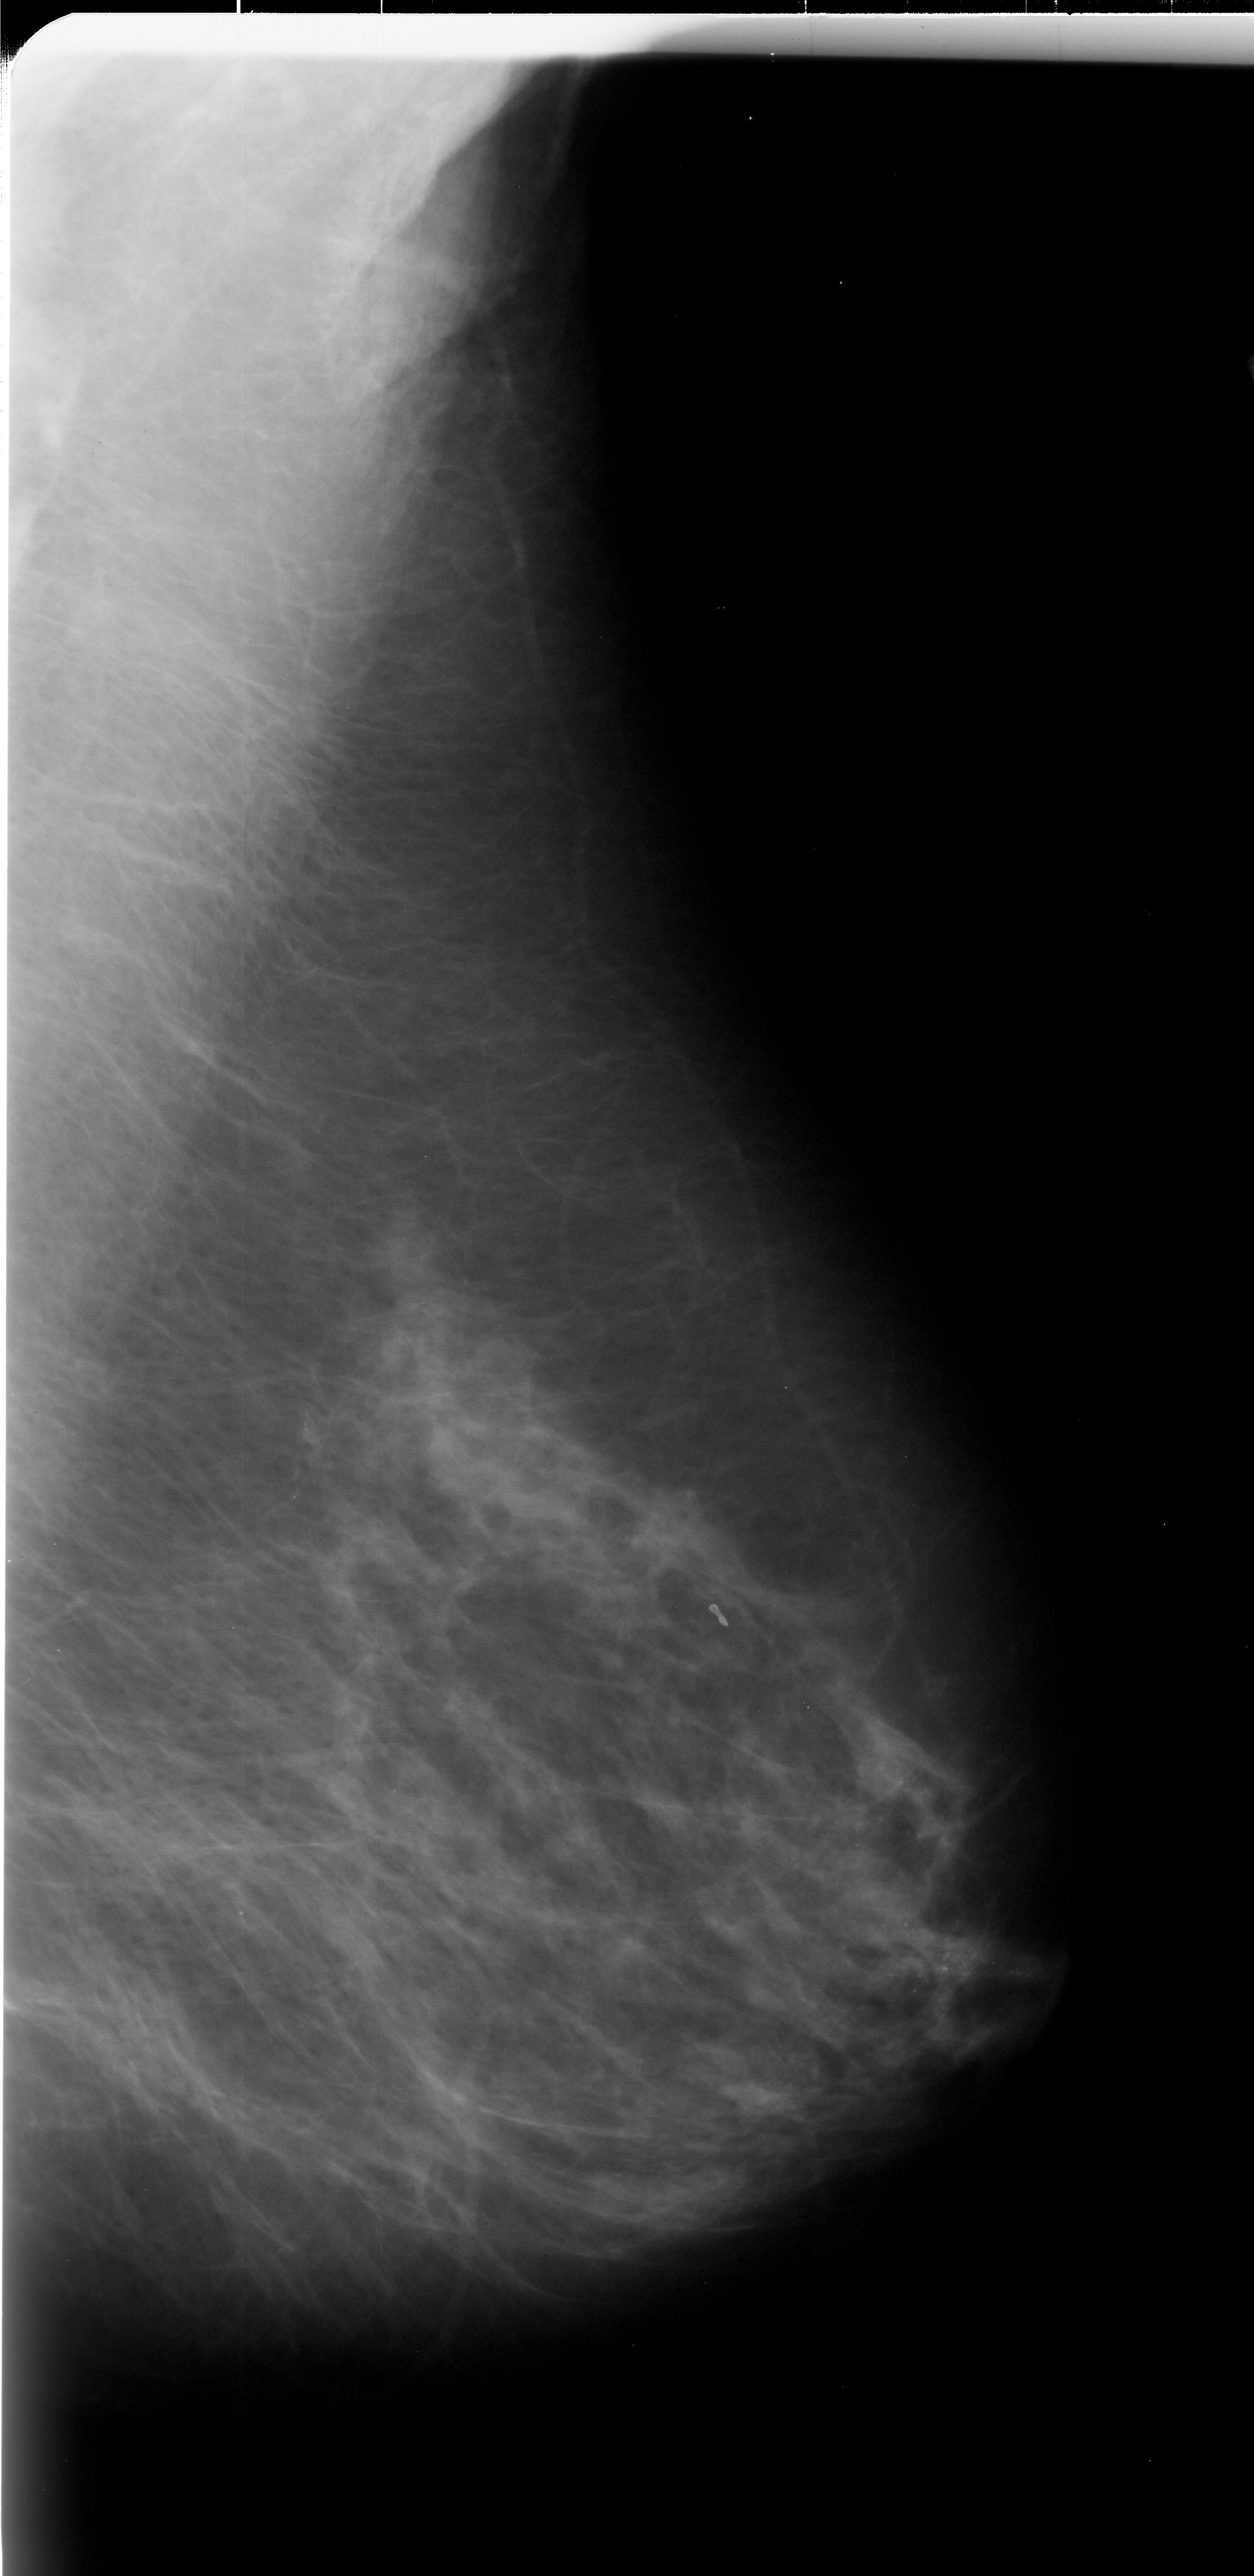
Scanned film-screen mammogram; right breast; mediolateral oblique (MLO) view; BI-RADS breast density category 2 (scale 1–4).
Calcifications, morphology fine linear branching, distribution linear; BI-RADS assessment category 5; subtlety rating 4 on a 1 (subtle) to 5 (obvious) scale; pathology (as recorded): malignant.